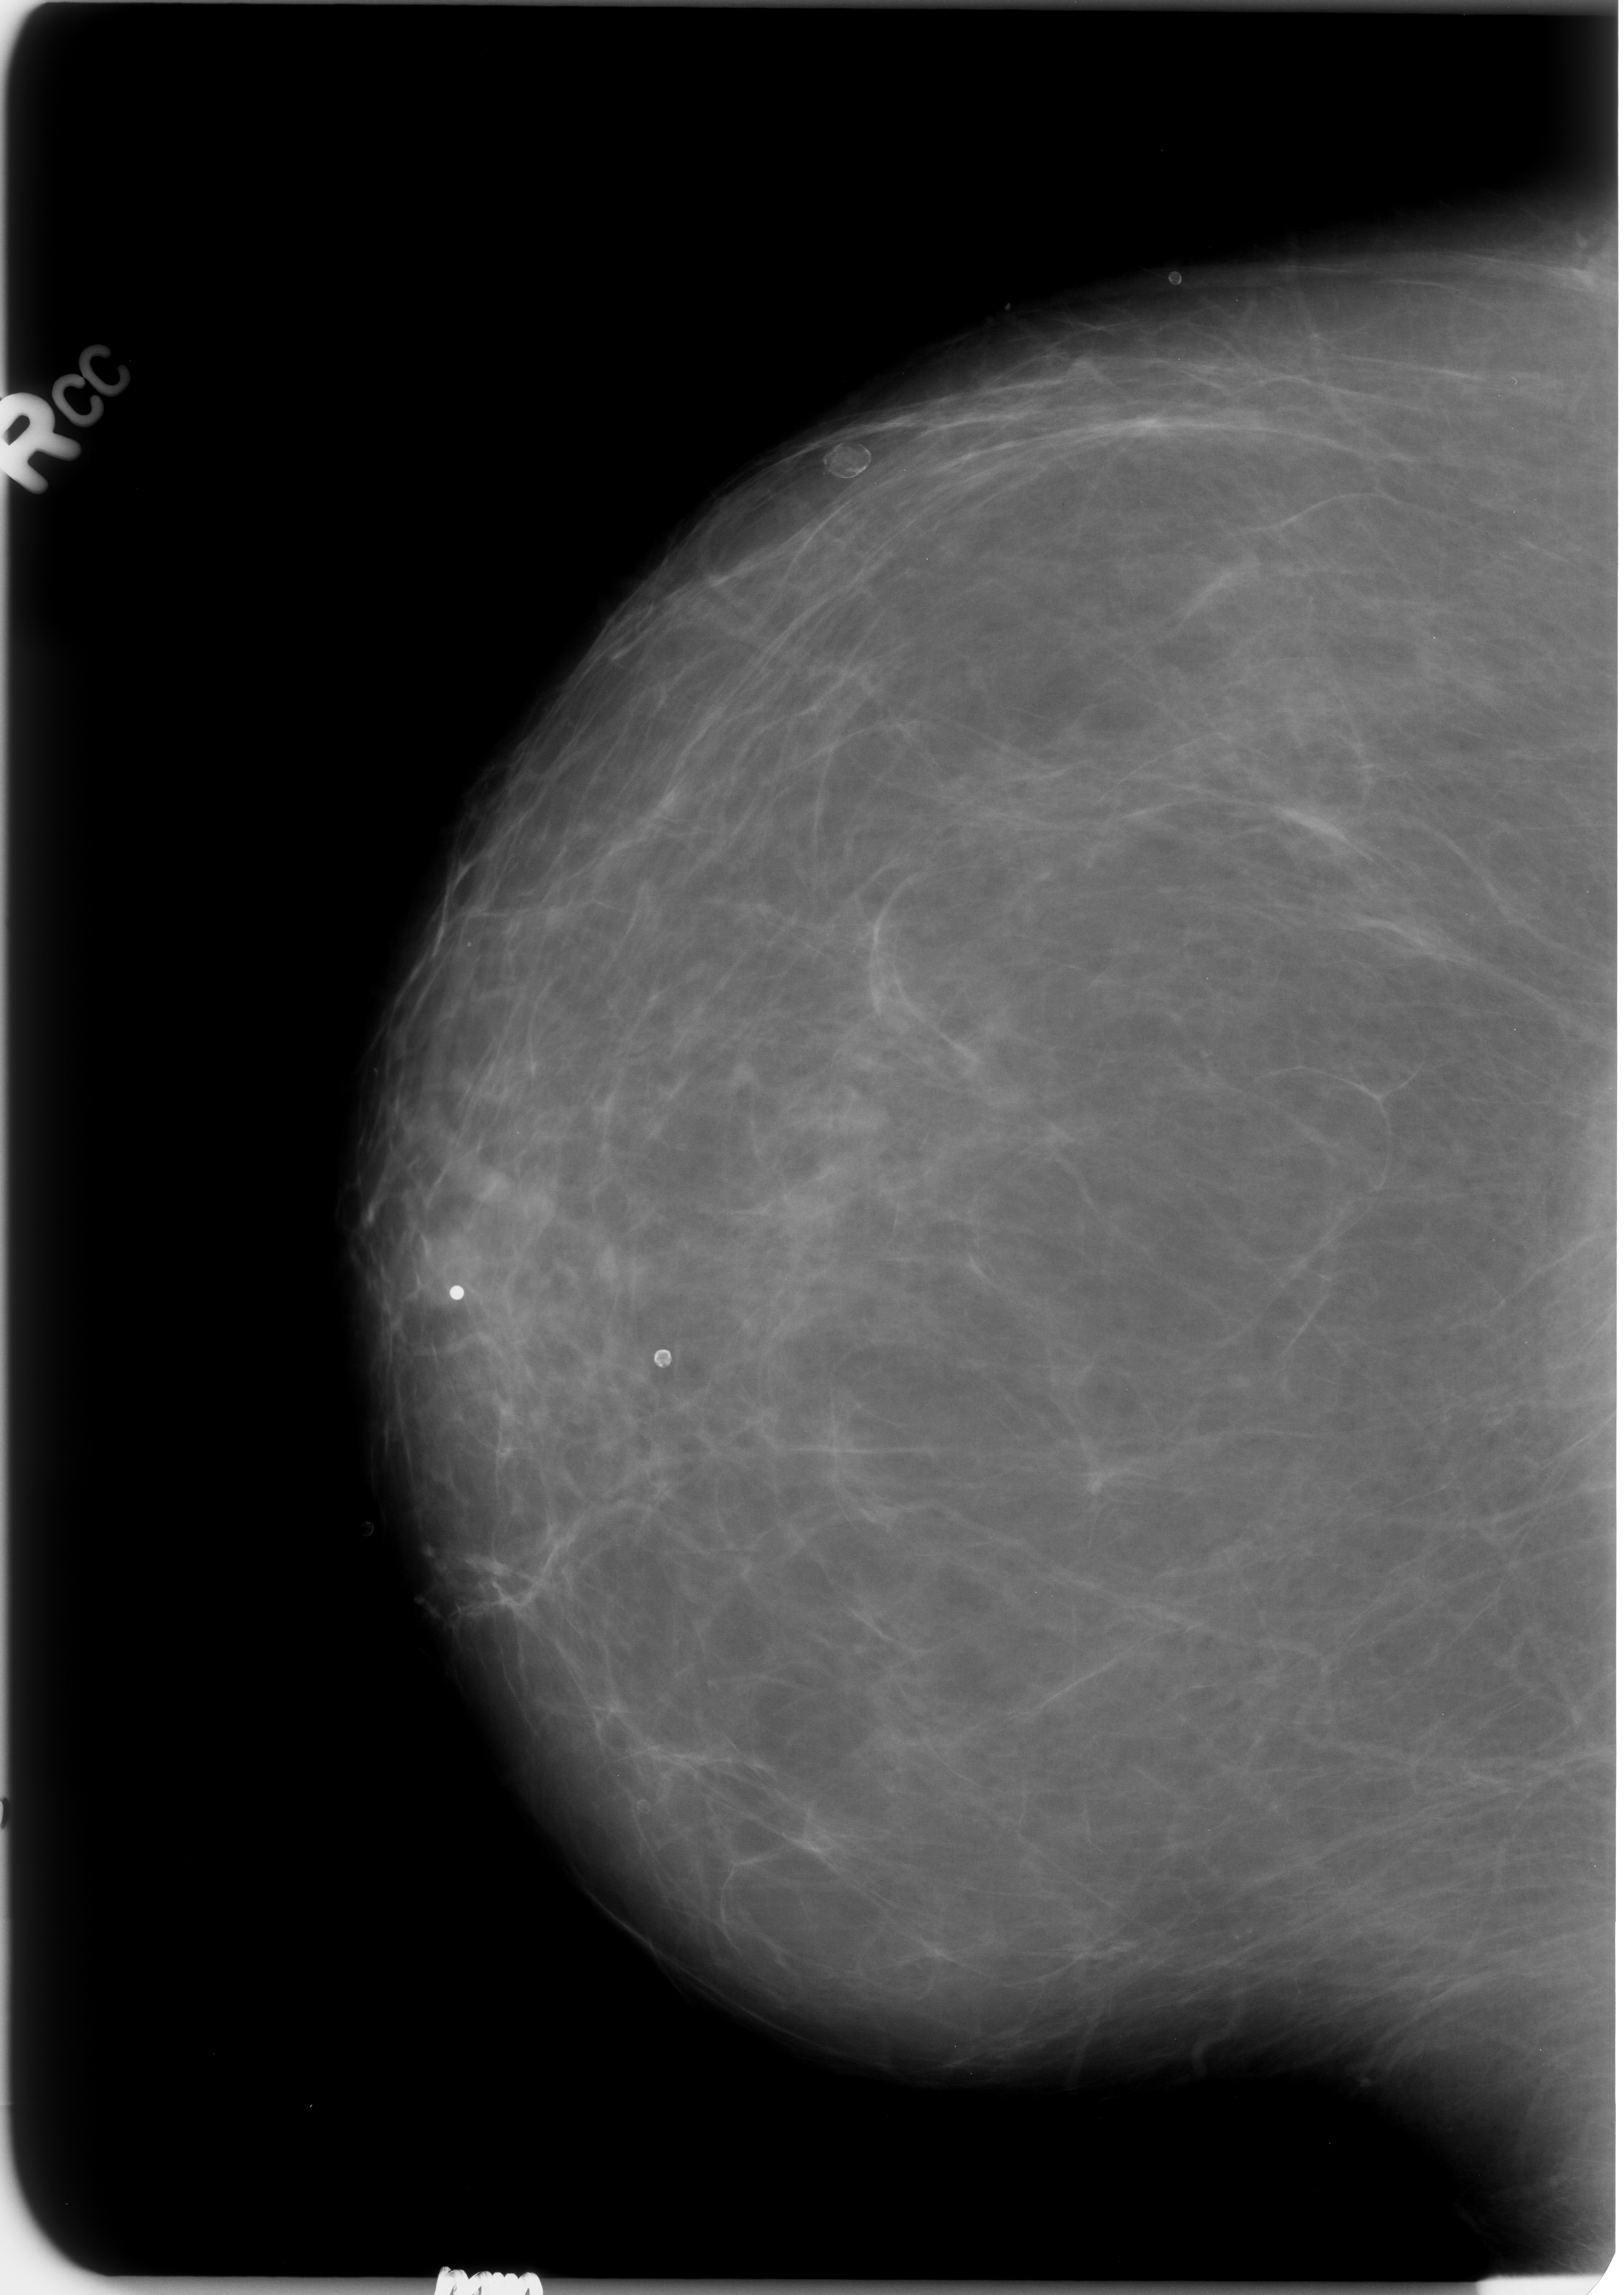
Scanned film-screen mammogram; right breast; CC view; BI-RADS breast density category 1 (scale 1–4); 1624 × 2295 image matrix.
Expert-marked regions of interest on this film, with their recorded descriptors:
- Finding 1 of 3: calcifications, morphology lucent center; BI-RADS assessment category 2; subtlety rating 5 on a 1 (subtle) to 5 (obvious) scale; outcome (as recorded, no biopsy): benign without callback (not worked up further): bounding box <645,1345,675,1381> (left, top, right, bottom; pixels)
- Finding 2 of 3: calcifications, morphology eggshell; BI-RADS assessment category 2; benign; no additional work-up was recommended (outcome (as recorded, no biopsy): benign without callback): <813,433,881,488>
- Finding 3 of 3: calcifications, morphology lucent center; BI-RADS assessment category 2; subtlety rating 5 on a 1 (subtle) to 5 (obvious) scale; benign; no additional work-up was recommended (outcome (as recorded, no biopsy): benign without callback): <1155,262,1188,295>